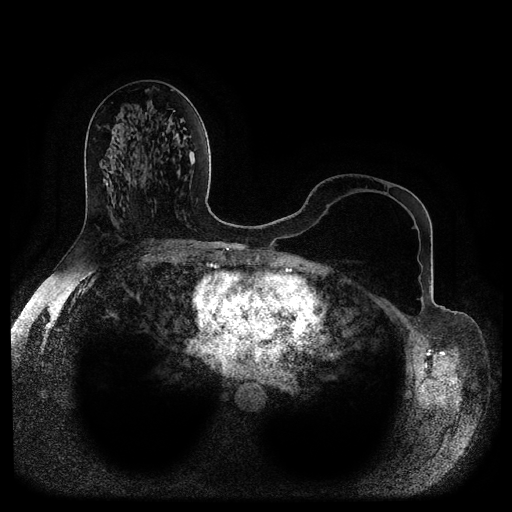
Breast MRI (dynamic contrast-enhanced, multi-phase), one axial slice; slice 50 of 116 in the series (ordered by position); dynamic contrast-enhanced series, time point 2 of 5 at this slice position (early post-contrast); 1.5 T; TE 2.6 ms, TR 5.2 ms; 2 mm slice thickness; 512 × 512 image matrix, field of view 380 × 380 mm. Female patient, age 56 years.
Structures marked on this image (semi-automatically segmented with operator editing):
- breast lesion (labelled benign in the annotation): bounding box (x1, y1, x2, y2) in pixels: (162, 134, 167, 140)